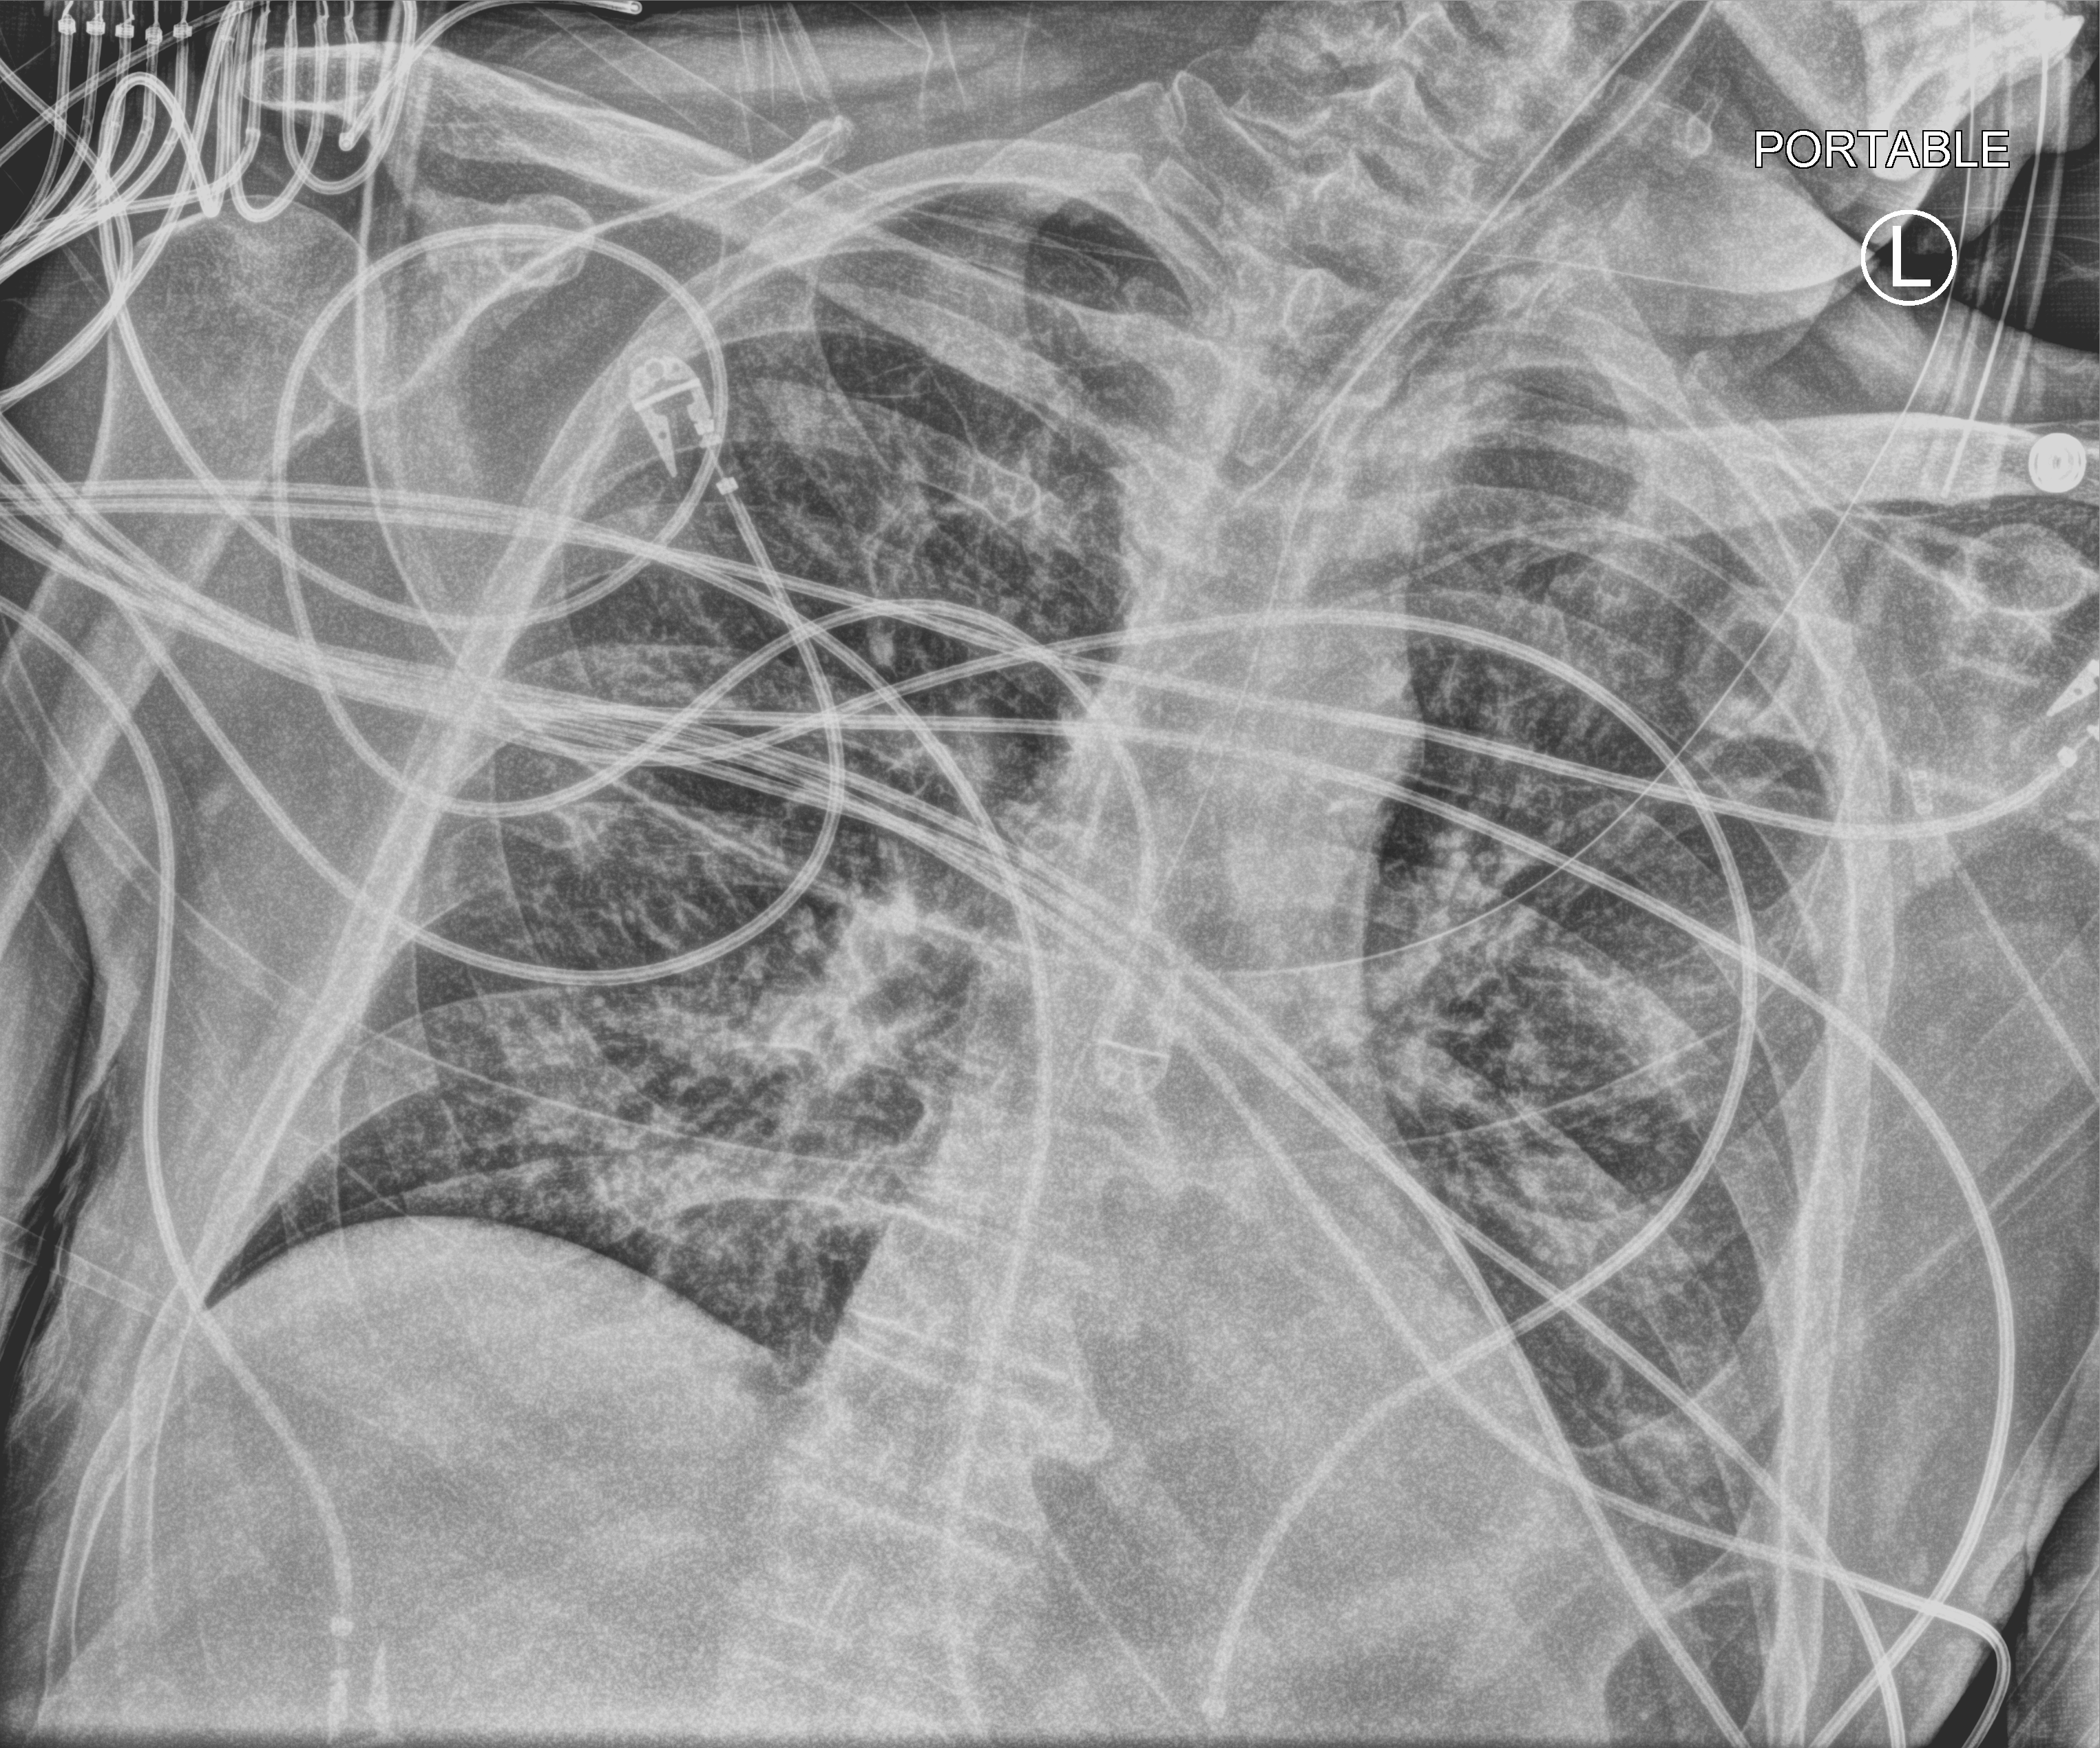
Chest X-ray (portable), anteroposterior (AP) projection. Patient hospitalised with COVID-19; male, aged 60–74 years.
Admission-level facts for this patient (not findings on this image; timing relative to this image not recorded):
- chronic kidney disease (admission record): no